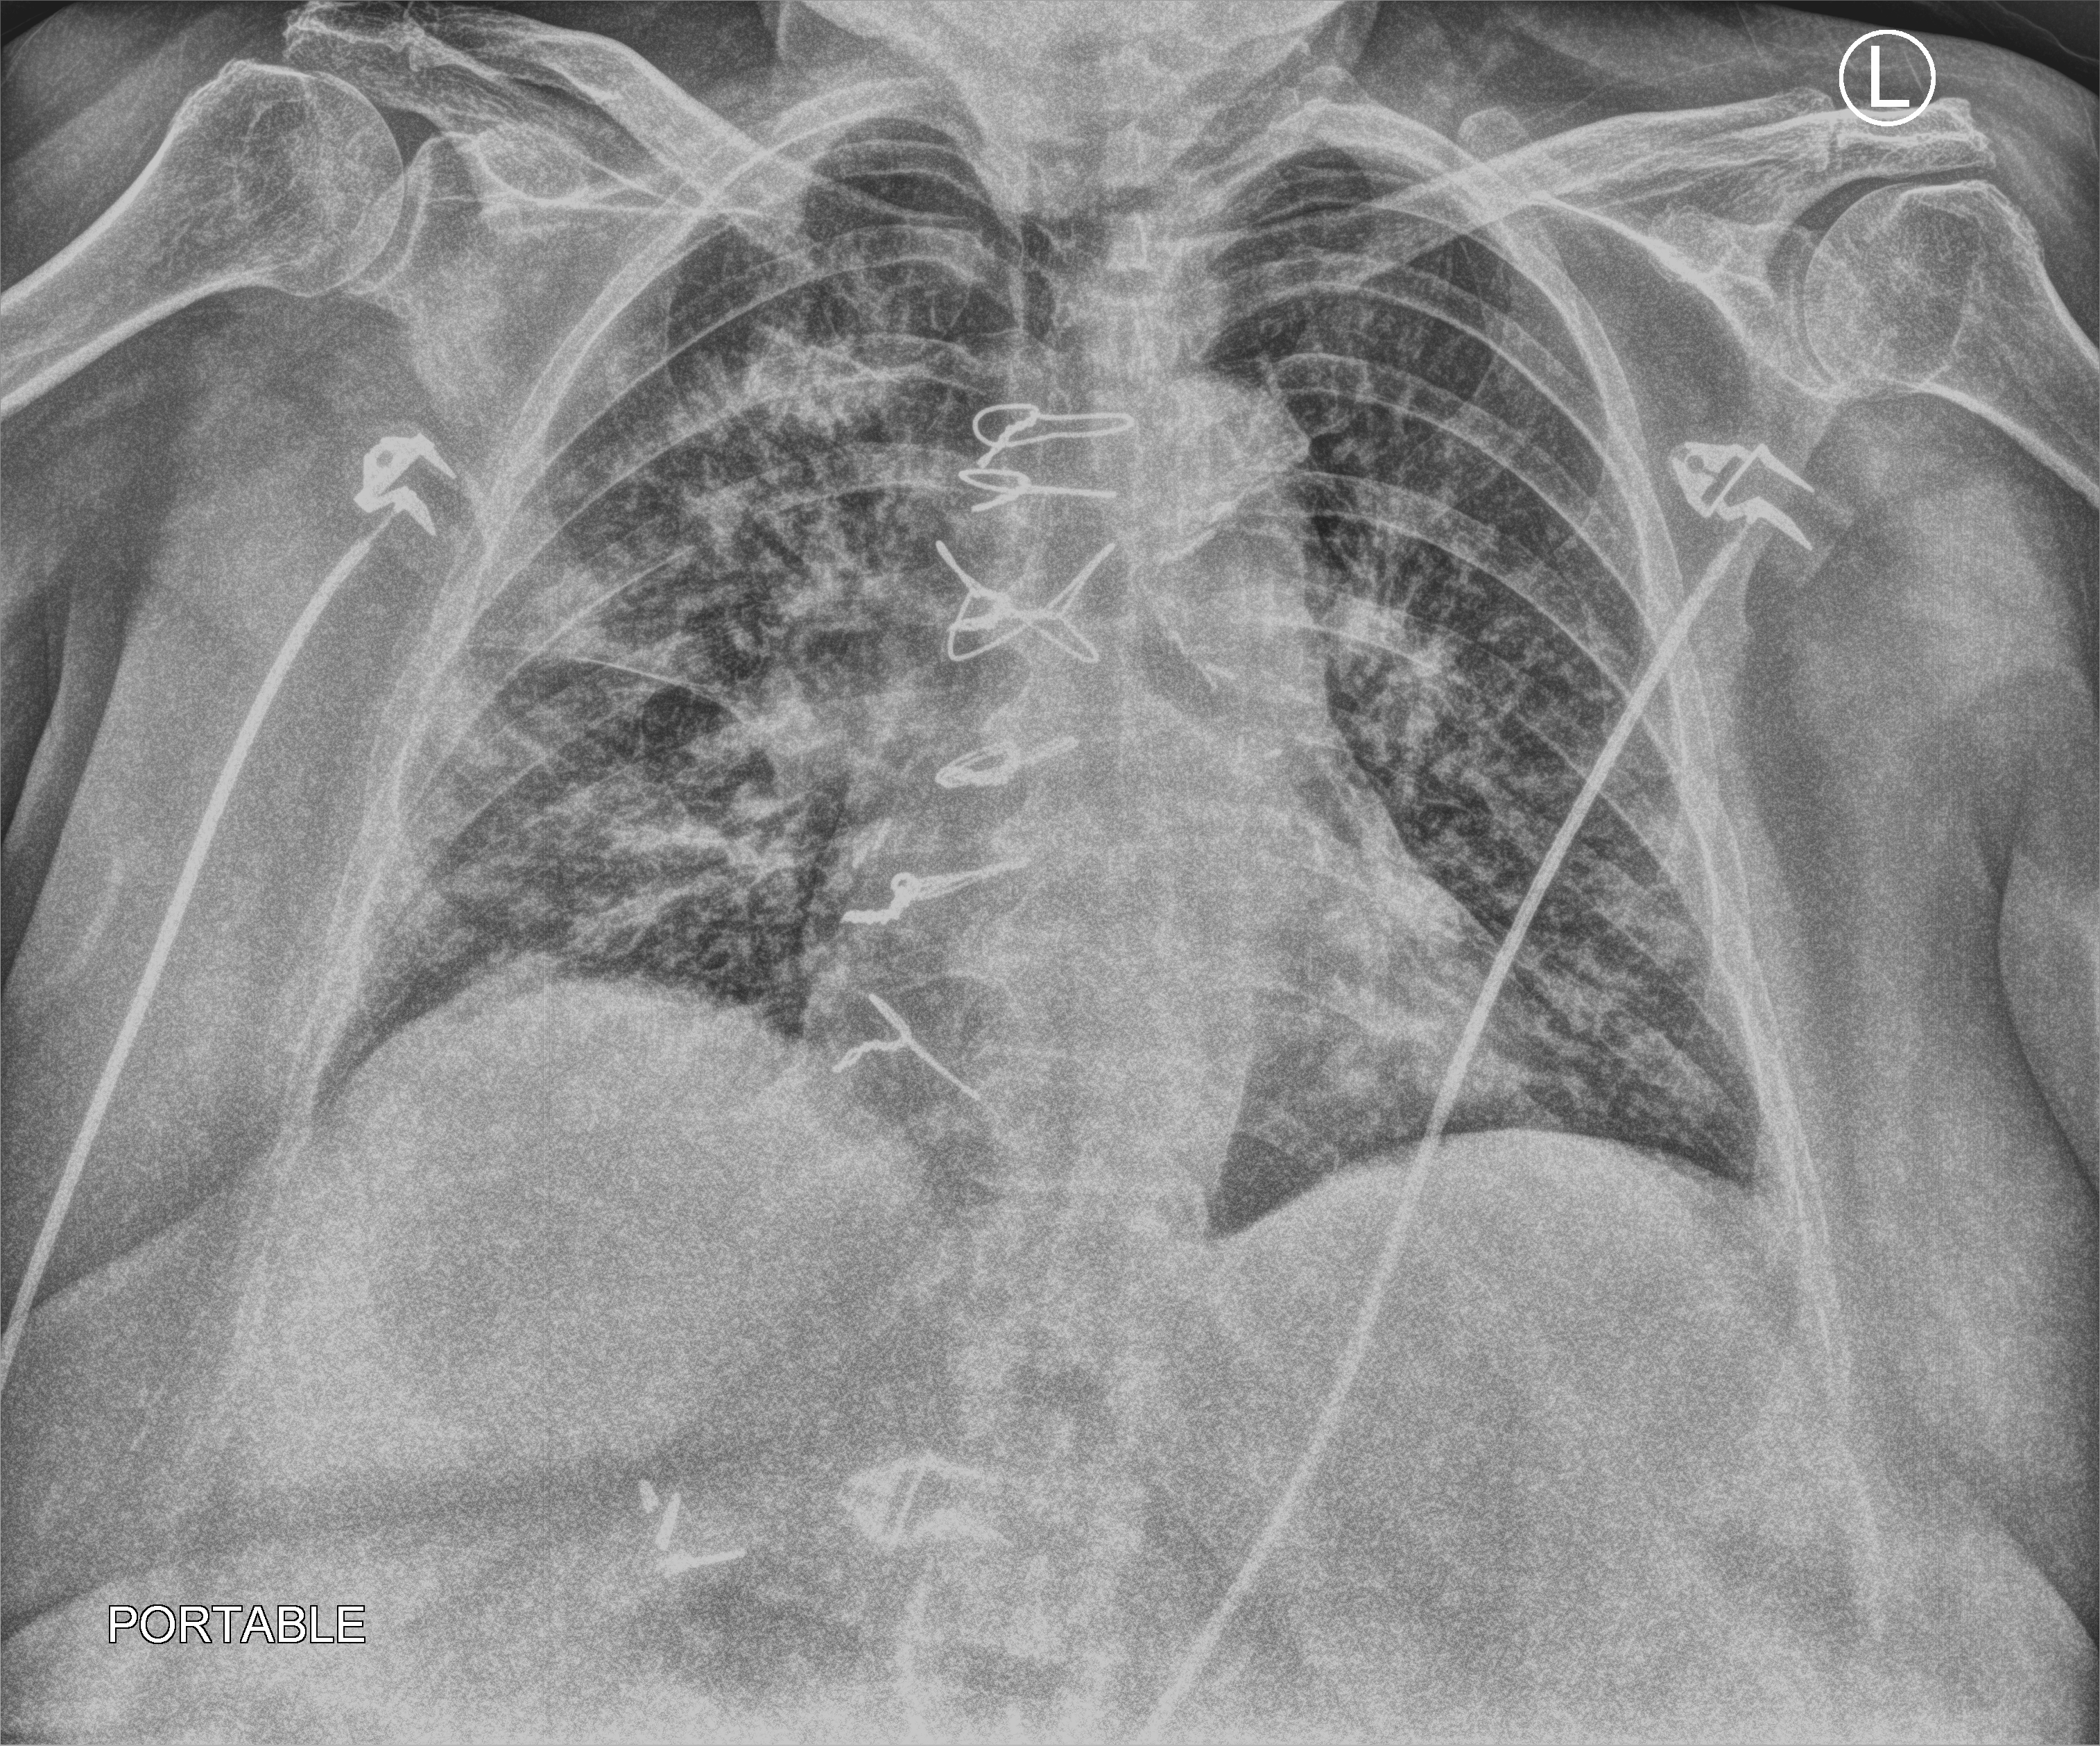
Chest X-ray (portable); anteroposterior (AP) projection. Female patient hospitalised with COVID-19, age 60–74 years.
Admission-level facts for this patient (not findings on this image; timing relative to this image not recorded):
- admitted to intensive care during this hospital stay: no
- mechanically ventilated during this hospital stay: no